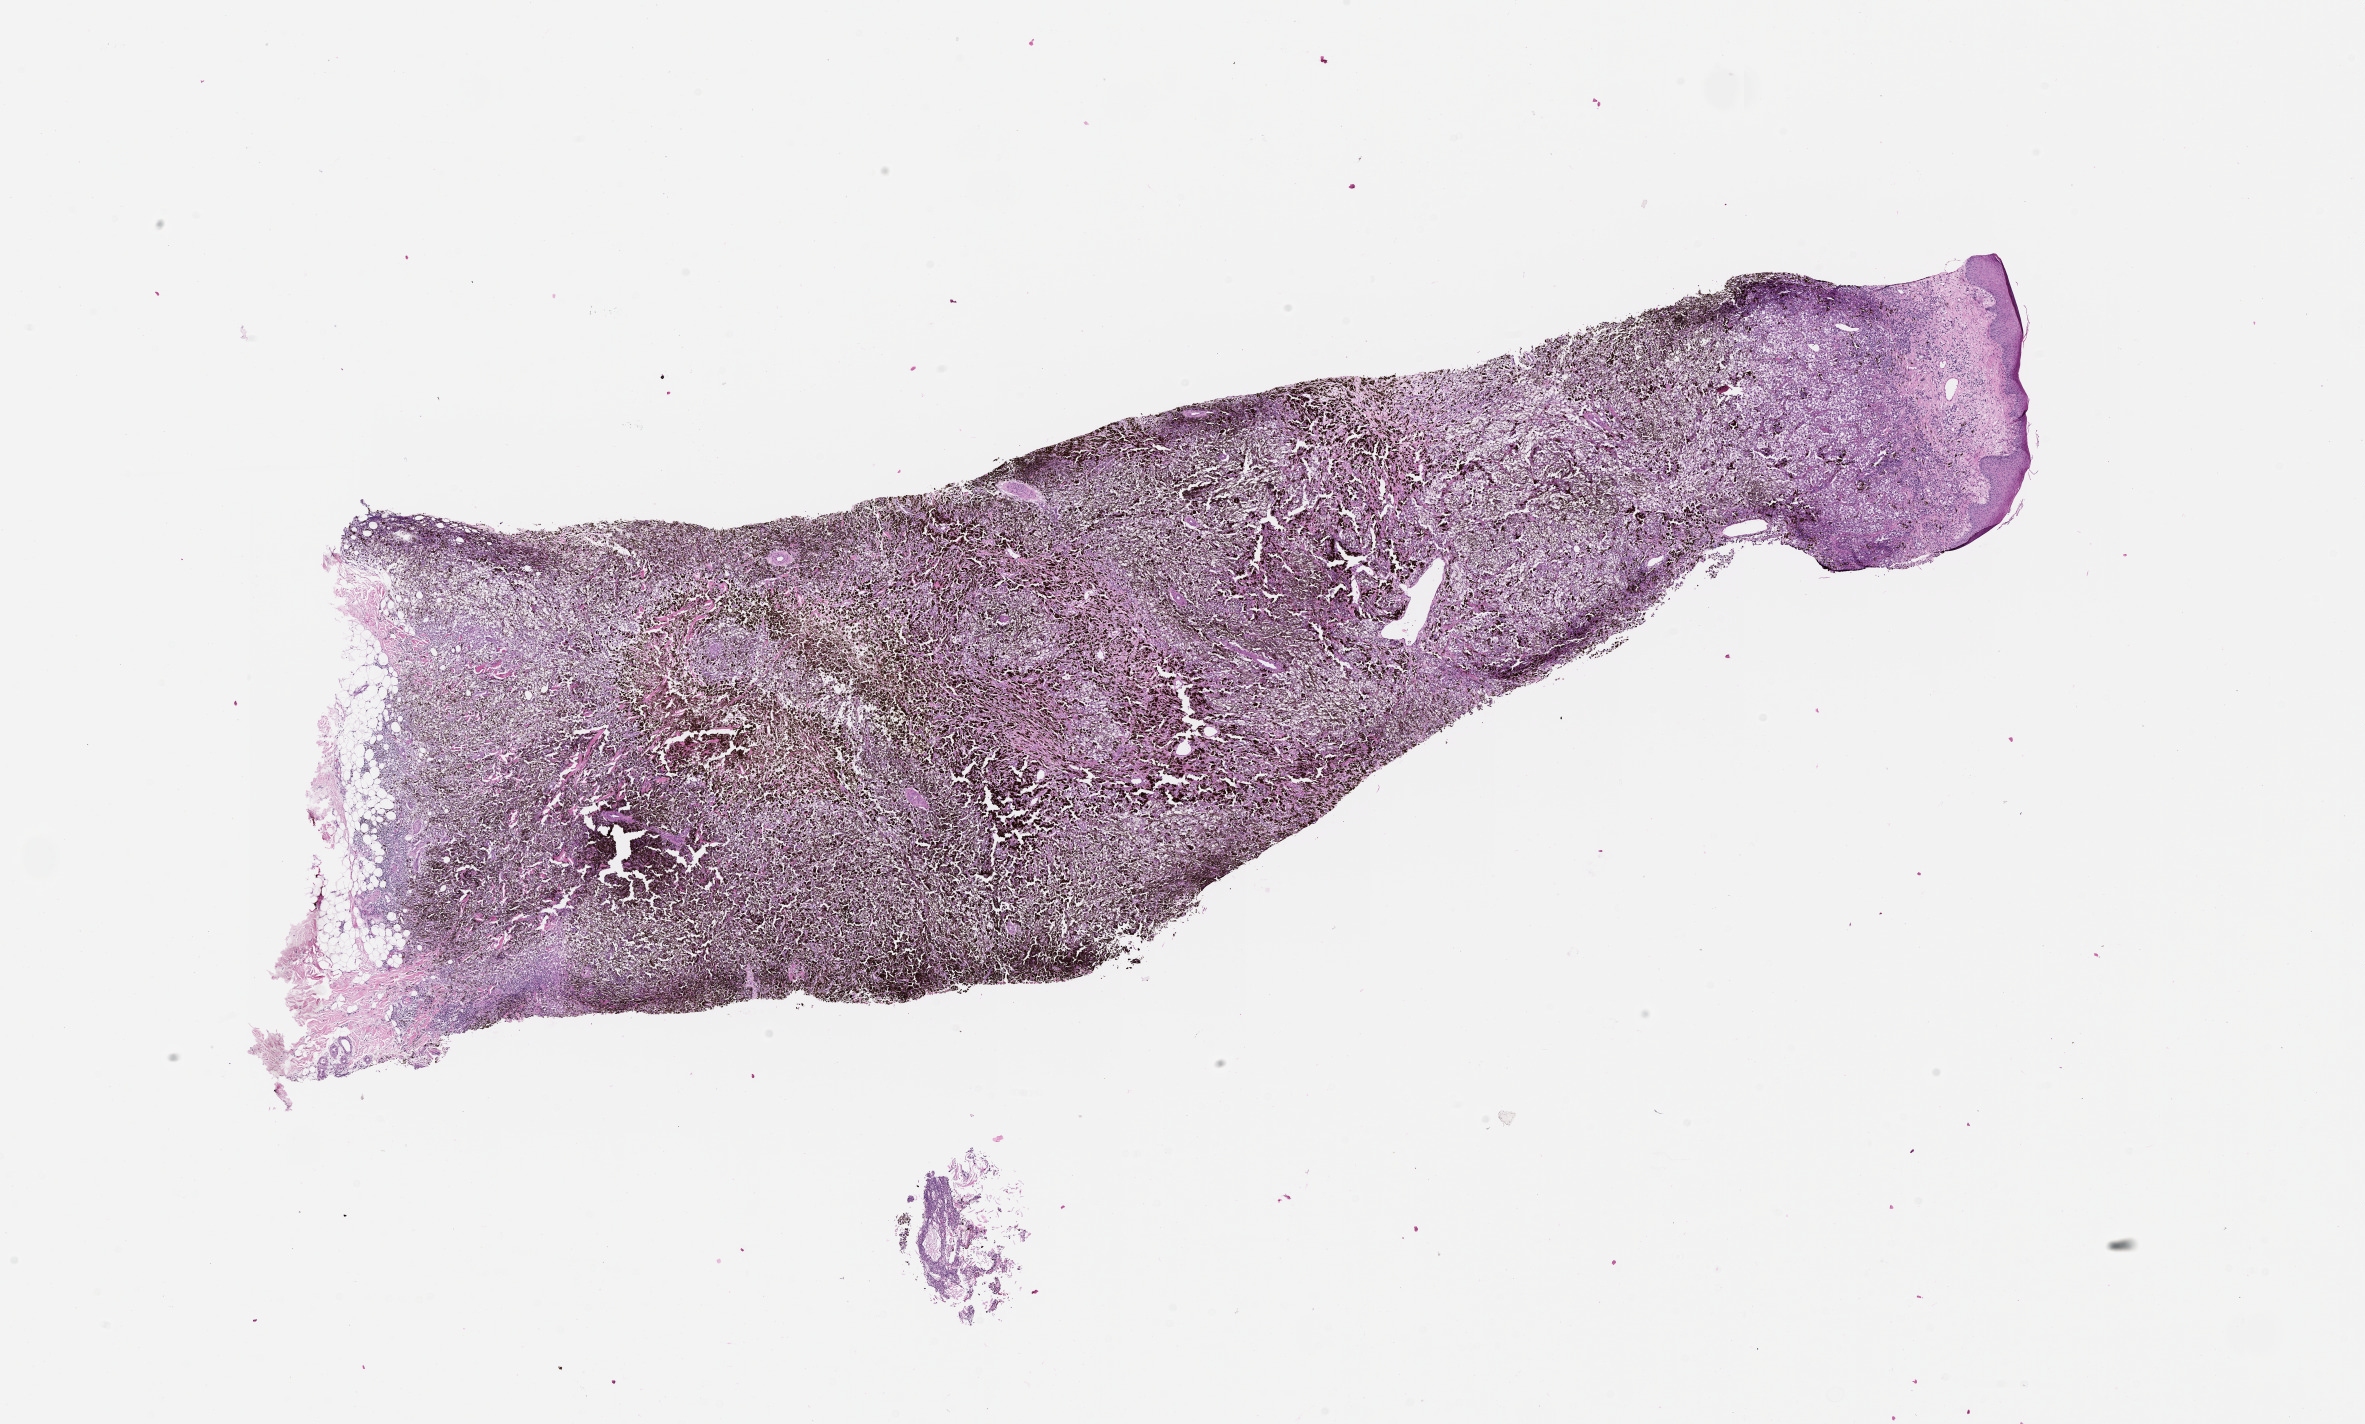
Digitized H&E tissue section (whole slide), low-resolution overview of the scanned area, about 19.0 x 11.5 mm (from a 20x scan); tumour tissue sample, sampled site: head & neck. 82-year-old female patient. Pathologist review of this section (percent, as recorded): tumour nuclei 80%, necrosis 0%.
Histologic diagnosis: Malignant melanoma, NOS.